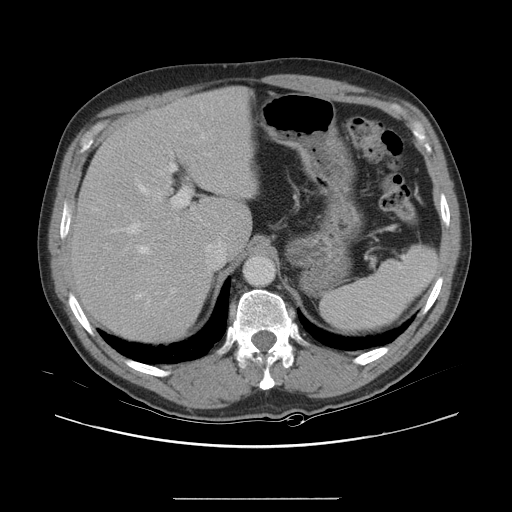
Contrast-enhanced abdominal CT, one axial slice. Position 19 of 40 along the scan axis. 120 kVp. Intravenous contrast given. Soft-tissue window (W 400 / L 40 HU). 512 × 512 image matrix, field of view 408 × 408 mm. Male patient, age 64 years. Case-level facts recorded for this patient, not image findings: diagnosis: colorectal cancer liver metastases, imaged before liver resection.
Annotated regions visible in this slice (outlined manually by an expert reader):
- hepatic veins: bounding box <136,185,221,304> (left, top, right, bottom; pixels)
- liver: <74,90,250,340>
- planned liver remnant (the part of the liver to remain after resection): <87,90,250,249>
- portal vein (with intrahepatic branches): <123,136,204,292>